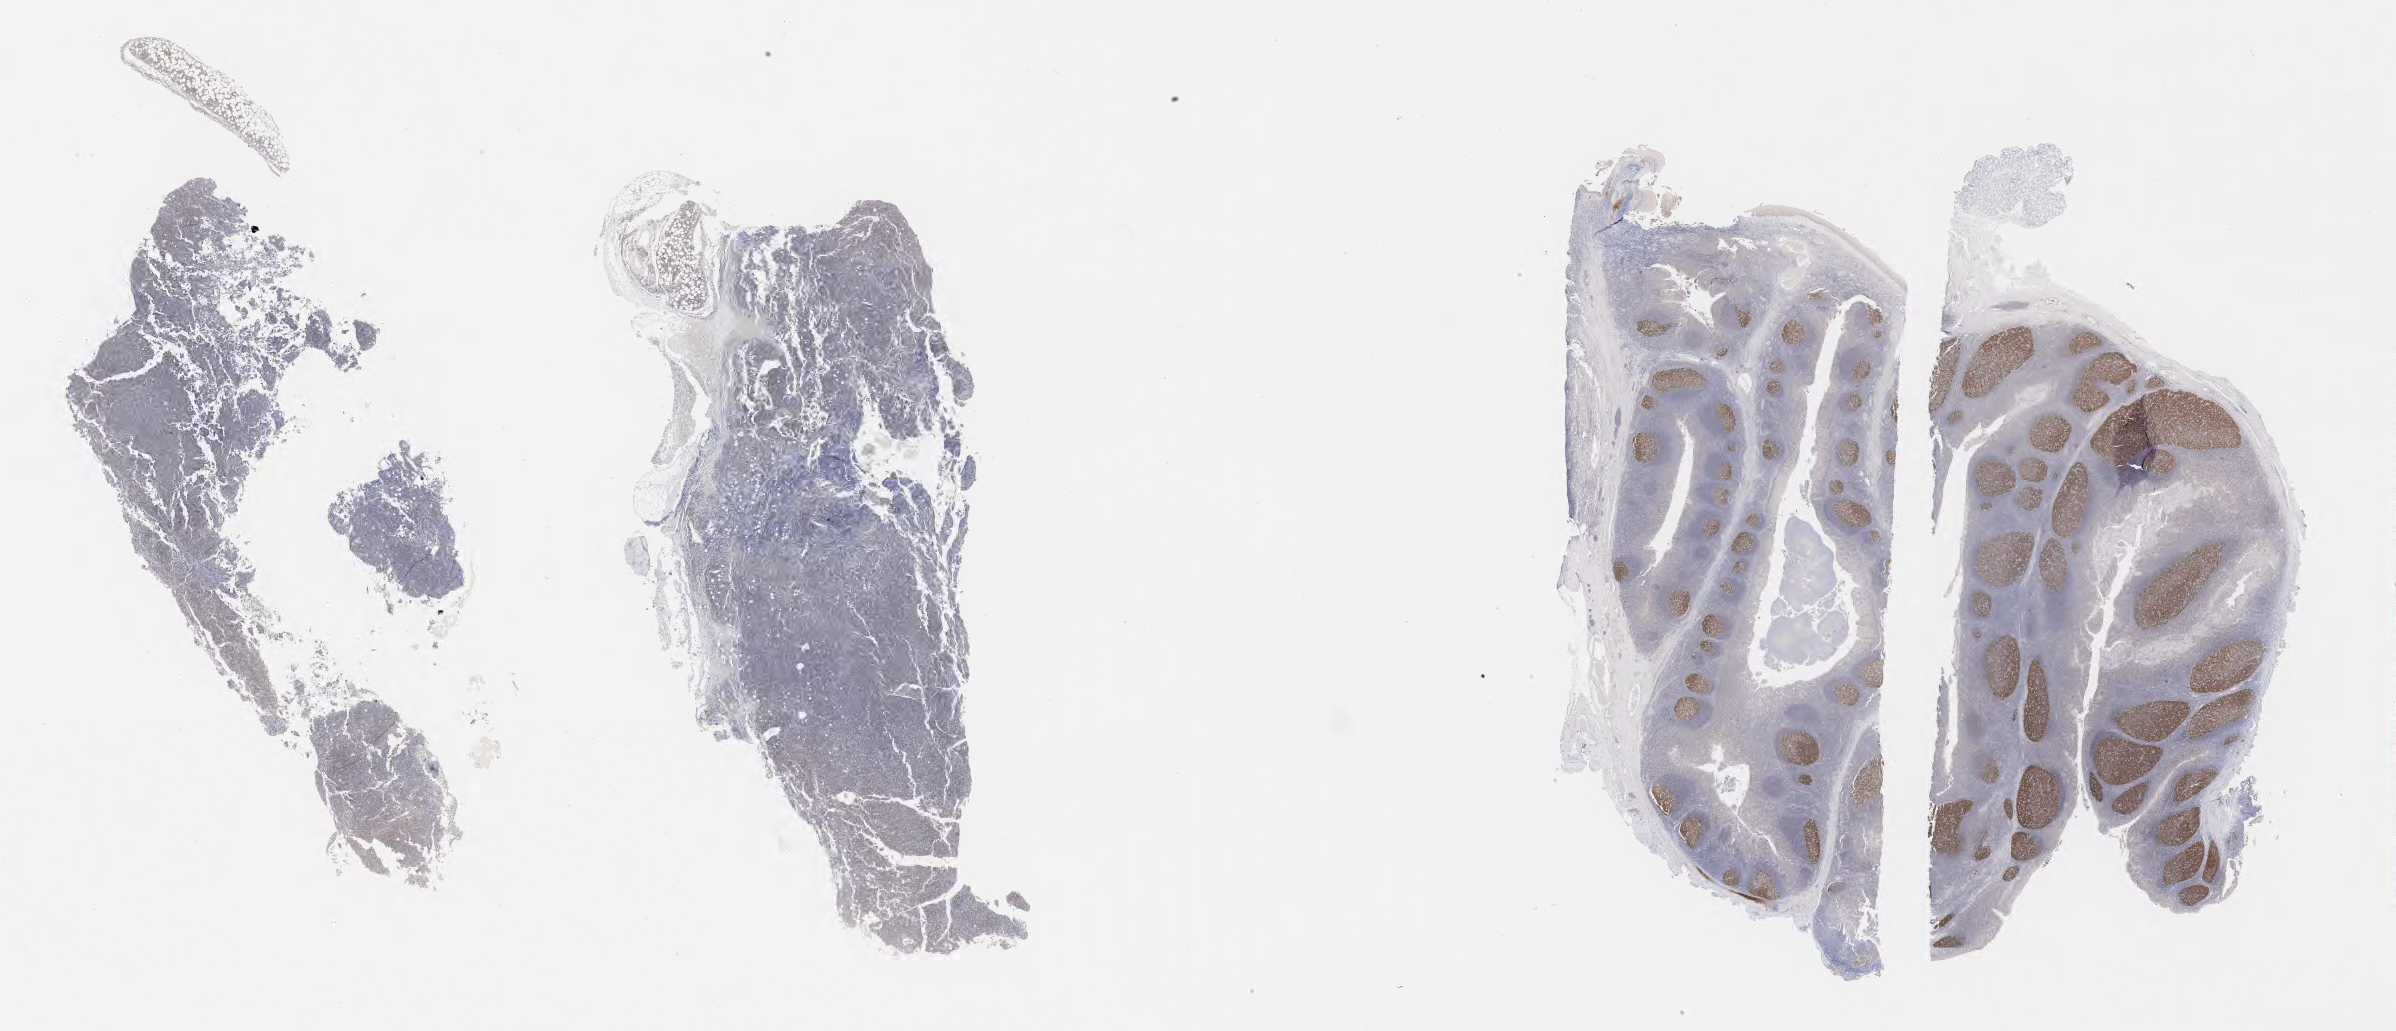
IHC for BCL6, whole-slide image — a low-resolution overview of the entire scanned area, about 38.7 x 16.7 mm. Specimen: tumor tissue. Female patient, 16 years old.
Histologic diagnosis: Burkitt lymphoma, NOS.